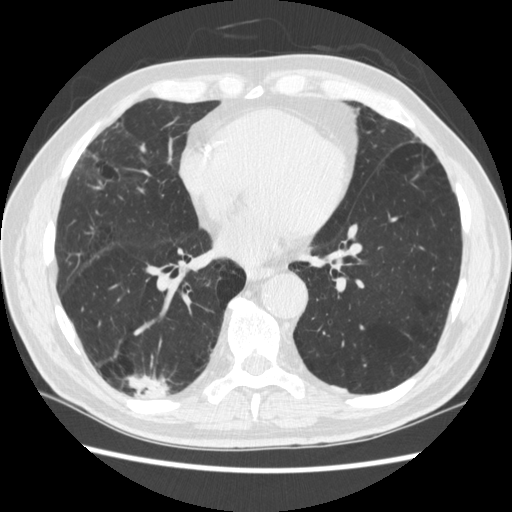
Axial slice from a low-dose chest CT screening exam. Third screening round (two years after baseline). Lung window (W 1500 / L -600 HU). 1.25 mm slice thickness. Slice 152 of 266 in the series. Male participant, aged 70 years at enrolment. Former smoker at enrolment.
Expert reader's lesion annotation, box from (x=125, y=360) to (x=181, y=417) px. The screening reader recorded 4 non-calcified nodules or masses ≥4 mm on this exam (right lower lobe, right lower lobe, left lower lobe, left lower lobe); which of them this box marks is not recorded. Official screen result: positive, other.